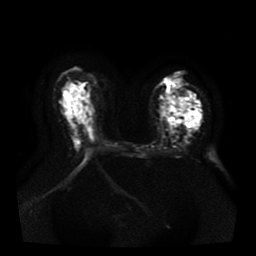
Breast MRI, one axial slice. Slice 25 of 41 in the series (ordered by position). Diffusion-weighted series; image 2 of 4 stored at this slice position (different b-values; order by instance number). 1.5 T. 5 mm slice thickness. 256 × 256 image matrix, field of view 330 × 330 mm. Female patient.
Annotated regions visible in this slice (outlined manually by an expert reader):
- tumour on diffusion-weighted imaging: box from (x=166, y=98) to (x=195, y=123) px